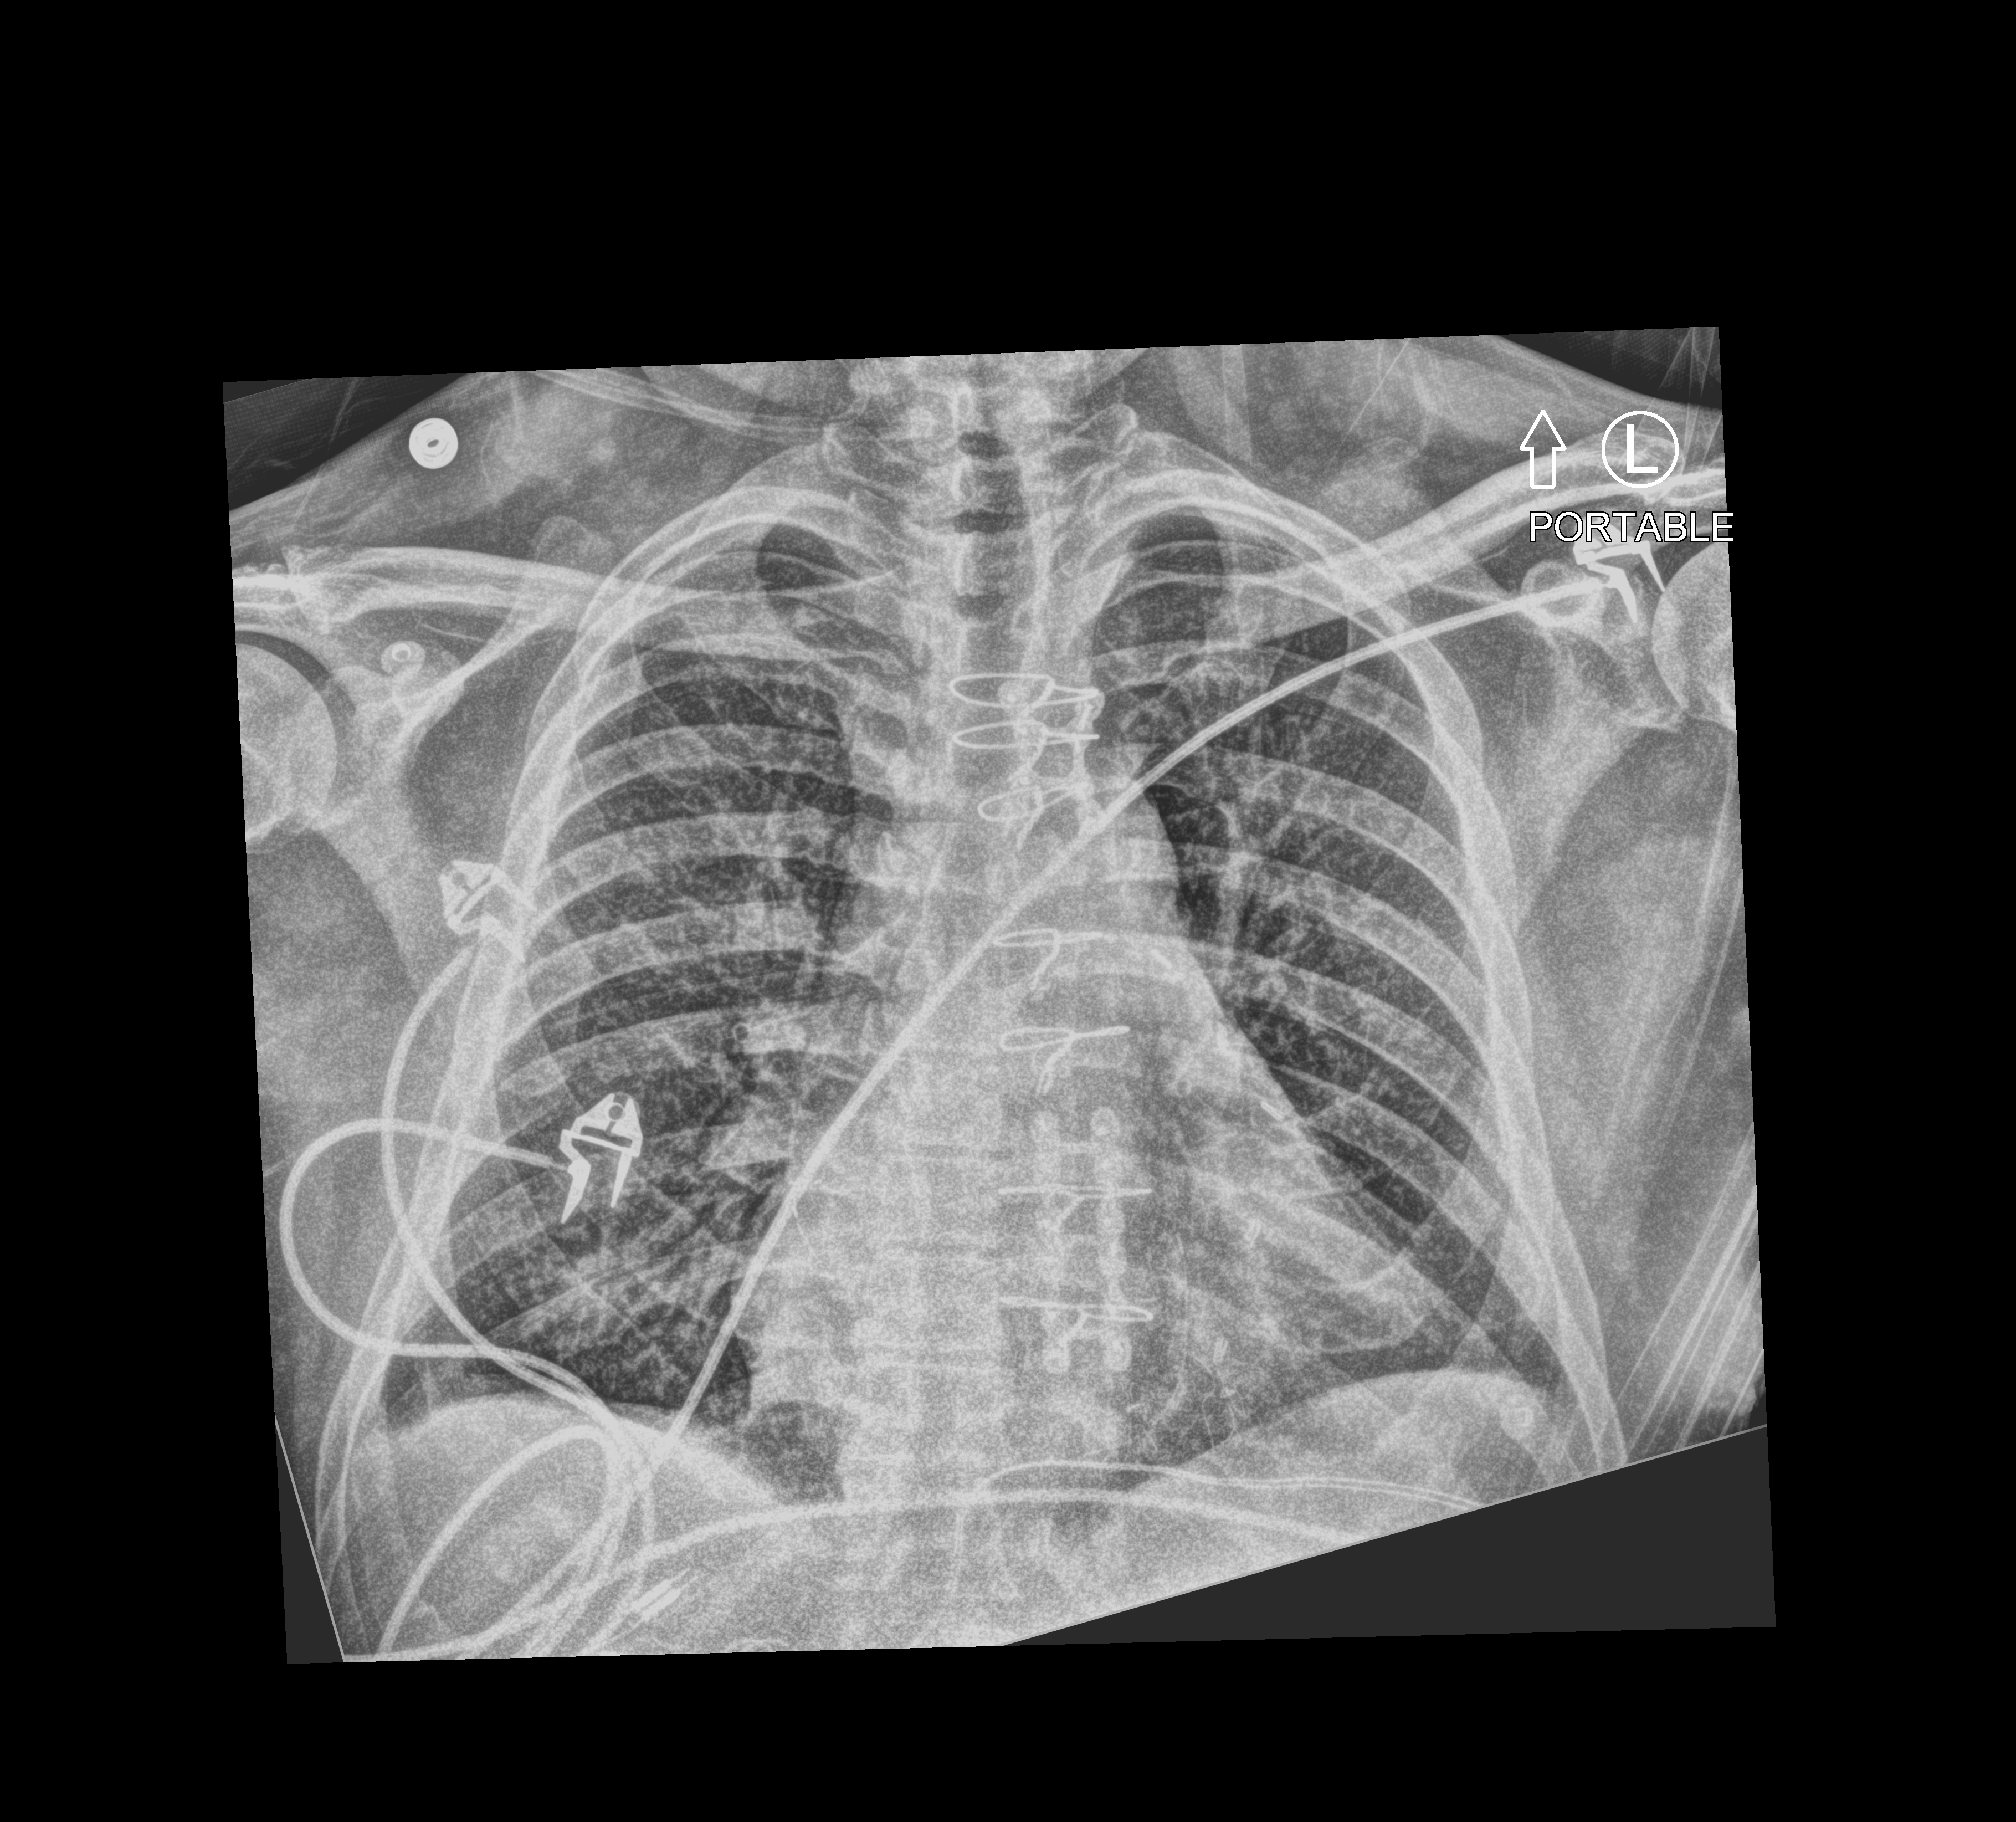
Bedside chest radiograph (computed radiography); anteroposterior (AP) projection. Patient hospitalised with COVID-19; male, aged 60–74 years.
From the hospital-stay record, not from the radiograph (when in the stay this image was taken is not recorded):
- length of hospital stay: 4 days
- chronic kidney disease (admission record): no
- COPD (admission record): no